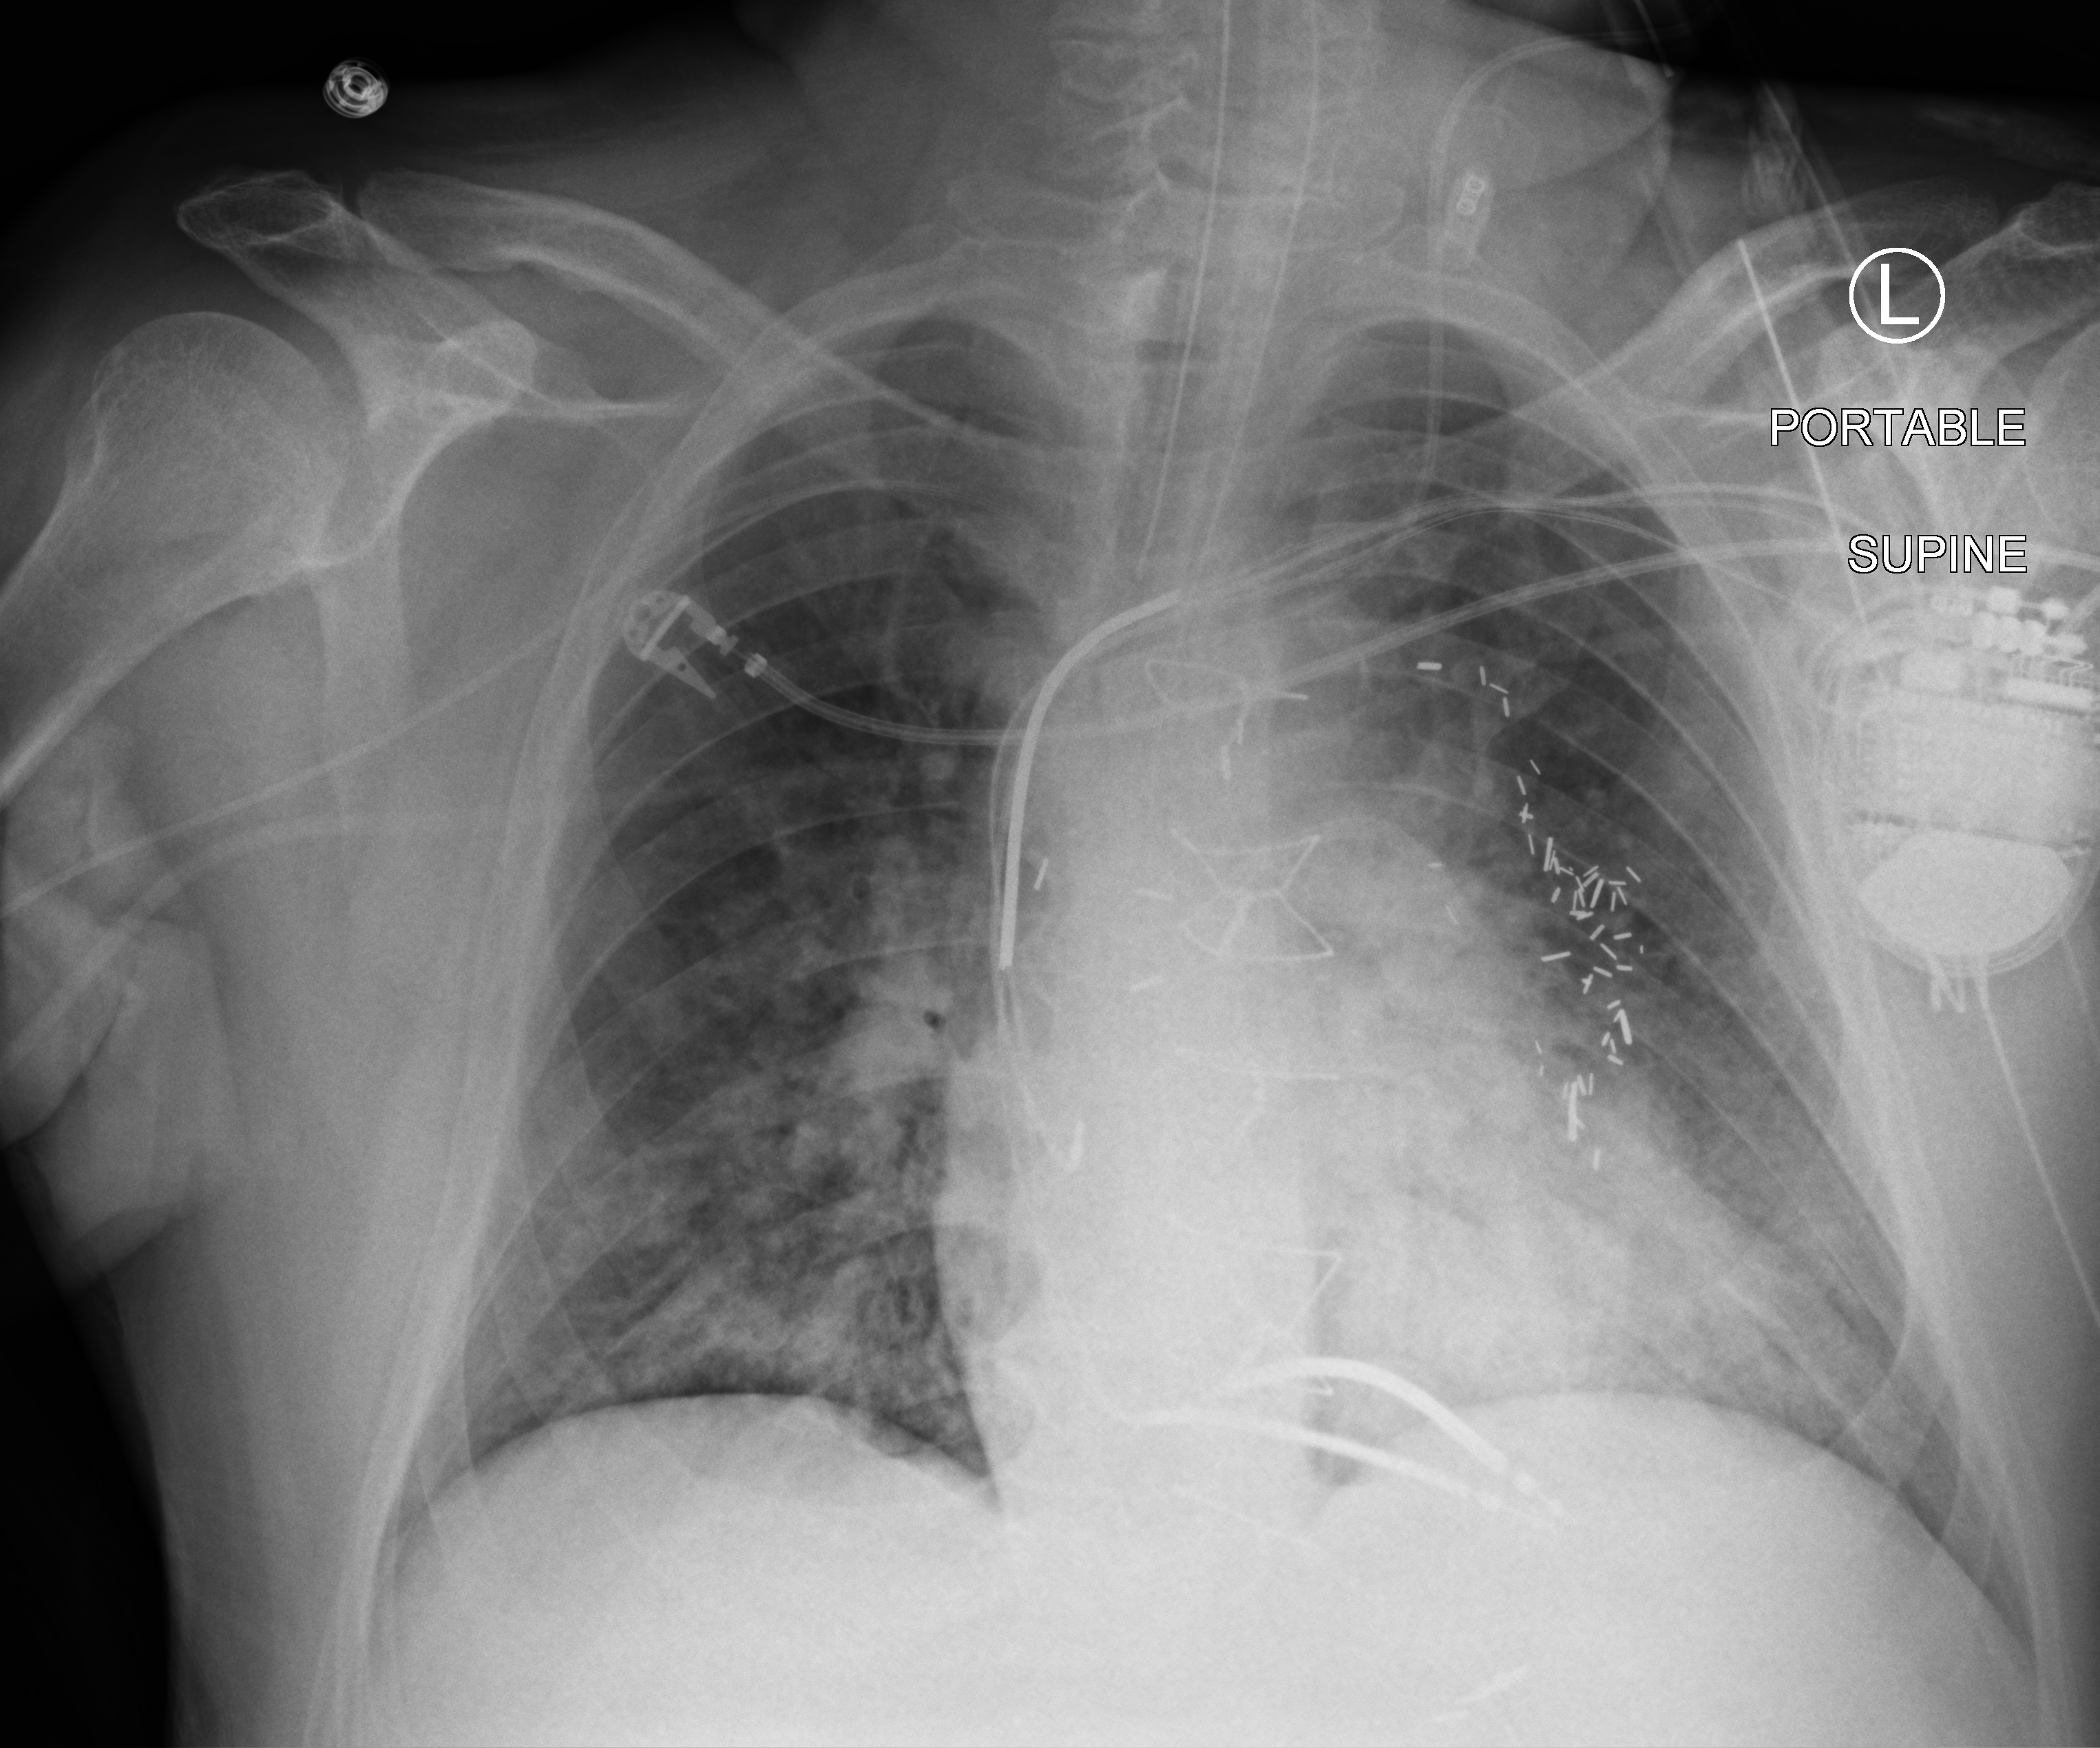
Chest X-ray (portable), anteroposterior (AP) projection. Patient hospitalised with COVID-19; male, aged 60–74 years.
Hospital-stay facts (about this admission, not read from this image; timing relative to this image not recorded):
- mechanically ventilated during this hospital stay: yes
- length of hospital stay: 55 days
- smoking status (admission record): never